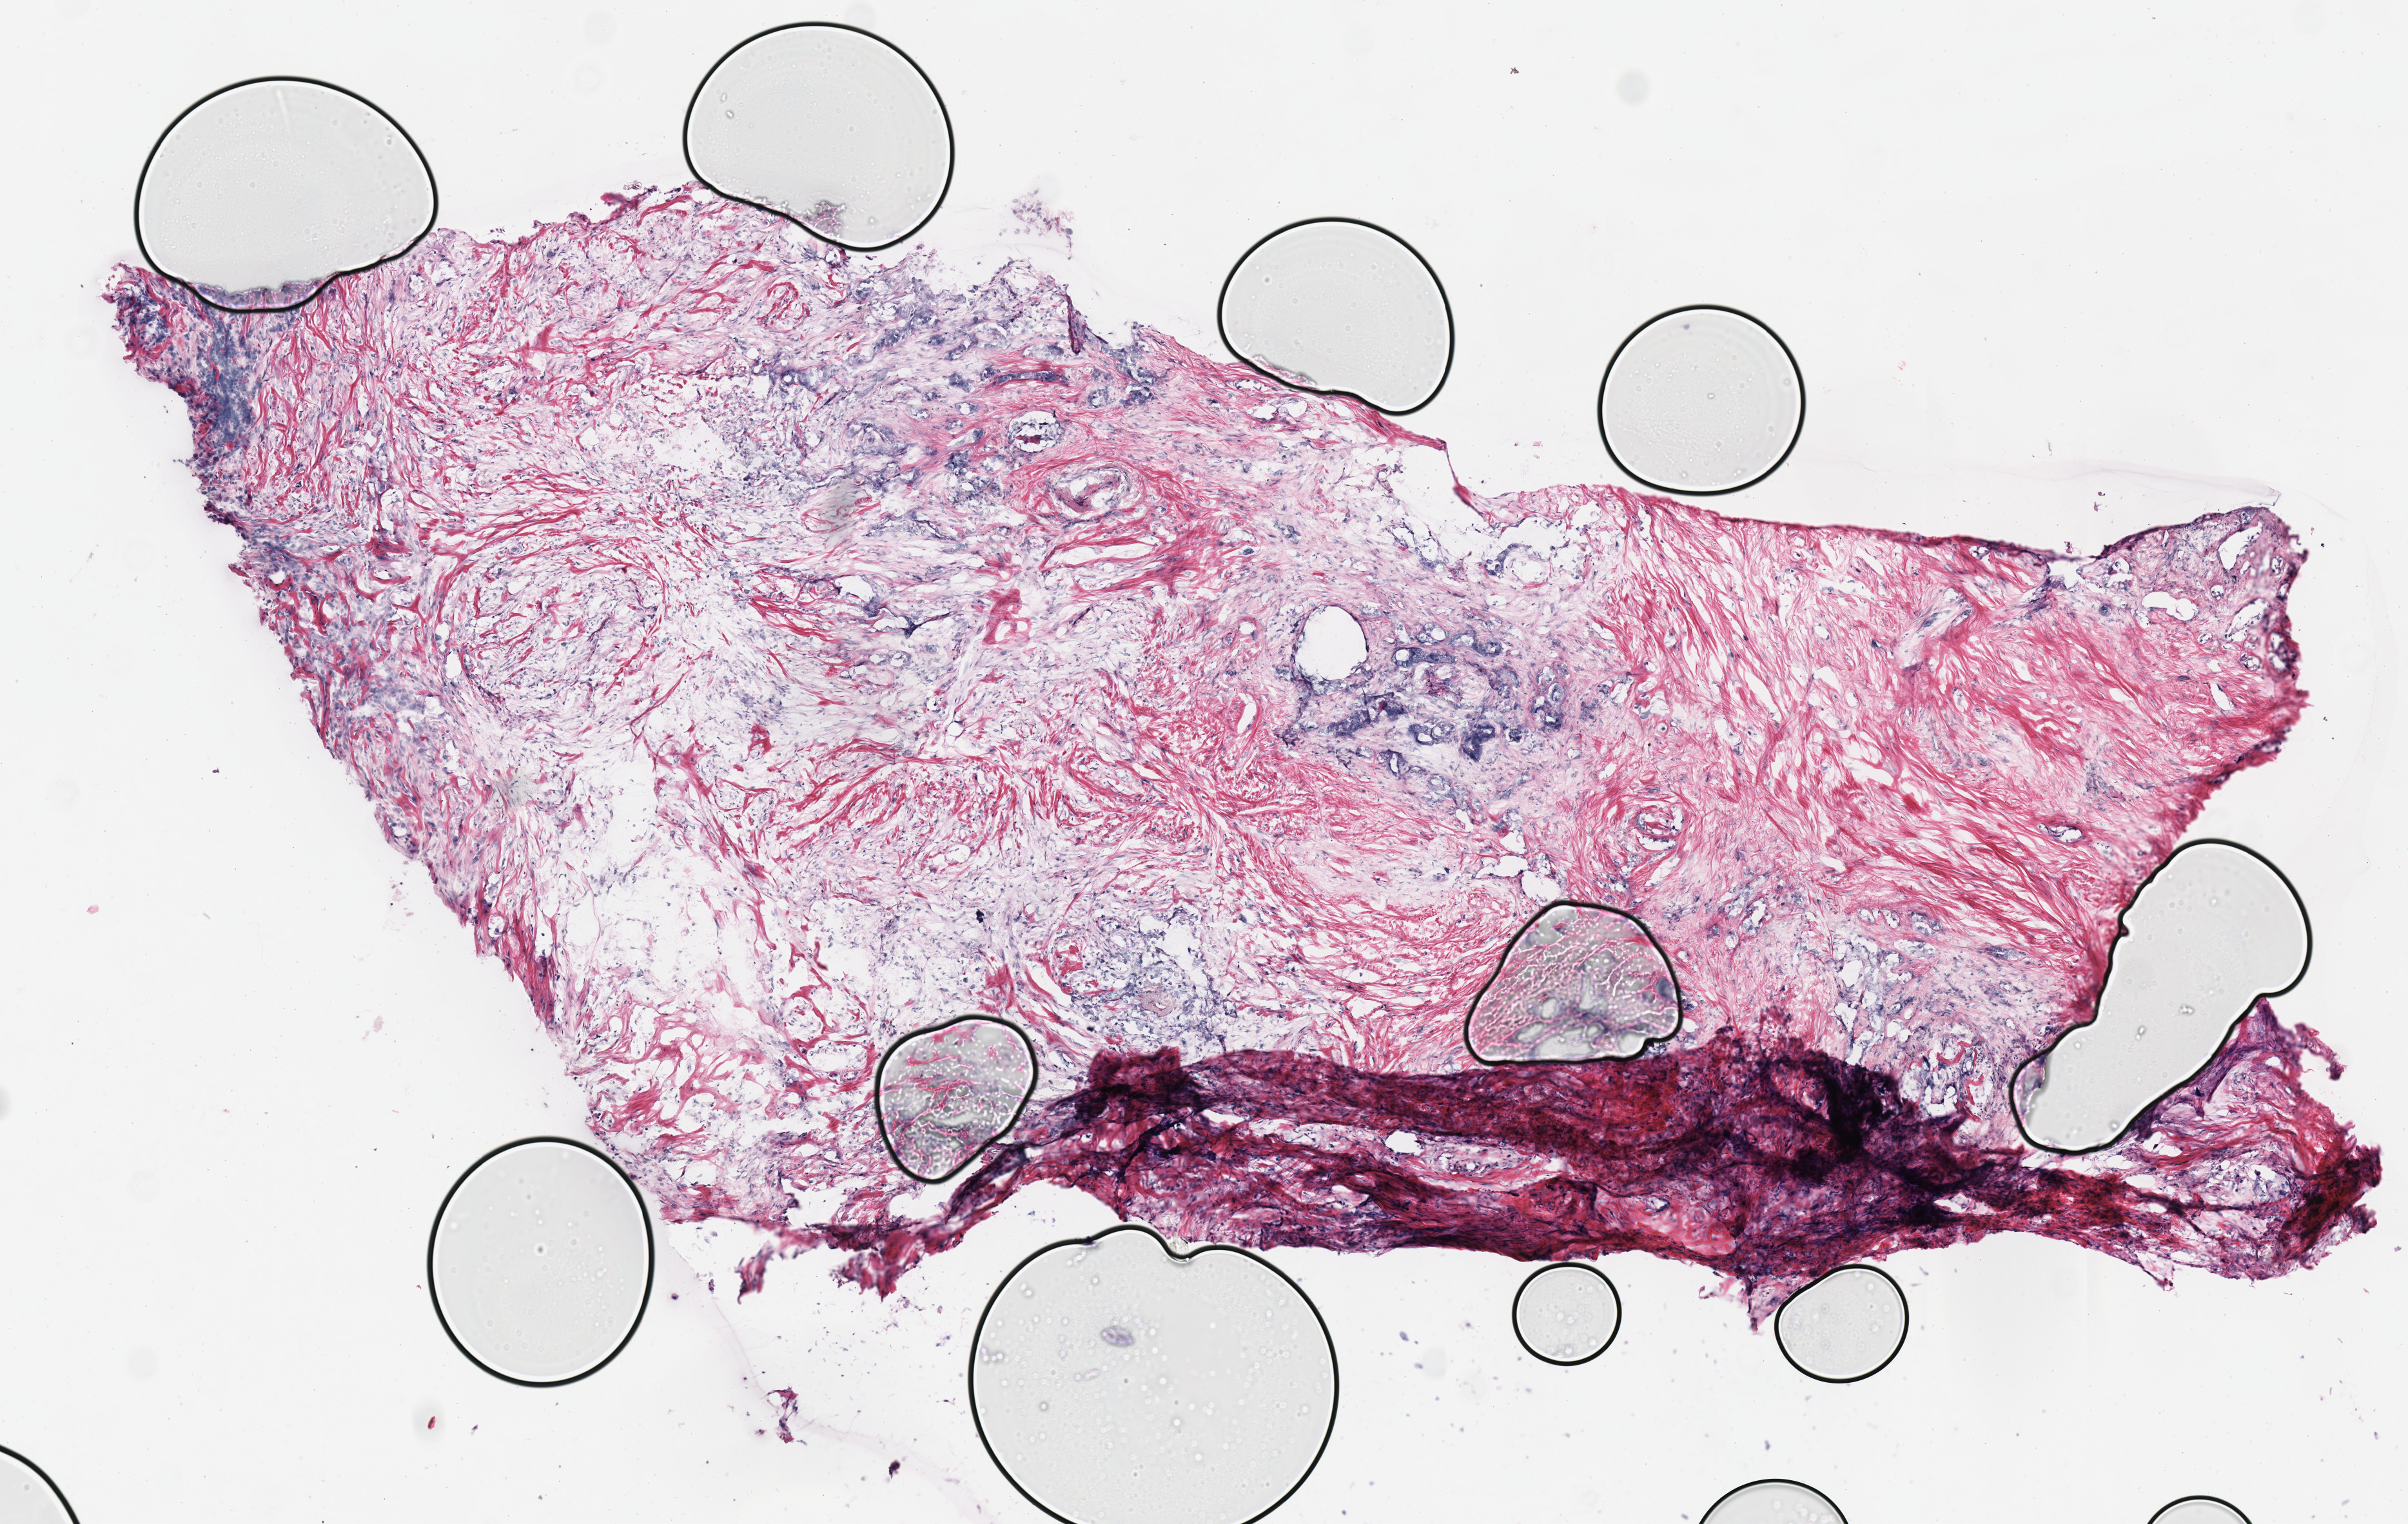
Hematoxylin and eosin (H&E) stained whole-slide image, shown as a low-resolution overview of the whole scanned area (about 7.3 x 4.6 mm), frozen section, primary tumour sample from the pancreas. Male patient; age at initial diagnosis 73 years. Histologic grade: G3 (poorly differentiated). Slide review estimates, as recorded: tumour cells 65%, tumour nuclei 70%, normal cells 0%, stromal cells 35%, necrosis 0%.
* AJCC pathologic stage: IB (6th edition)
* TNM: T2 N0 M0
* lymph nodes positive (case pathology): 0 of 11 examined
* pathologic diagnosis: Infiltrating duct carcinoma, NOS